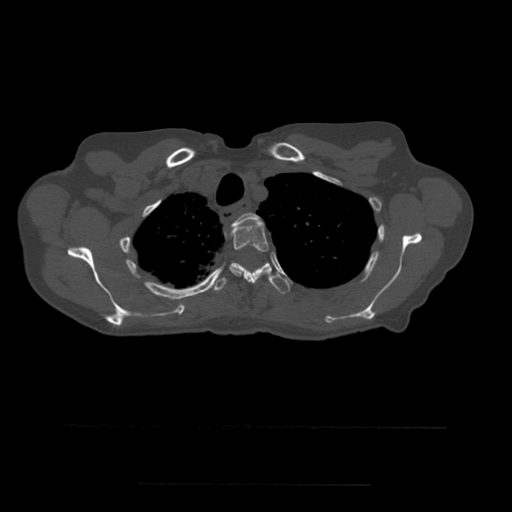
CT including the spine, one axial slice. Slice 417 of 544 in the series (ordered by position). Bone window (W 1800 / L 400 HU). 1.25 mm slice thickness. 512 × 512 image matrix, field of view 350 × 350 mm. Patient age 58 years. Case-level facts recorded for this patient, not image findings: primary cancer: lung.
Outlined on this slice (semi-automatic segmentation, software-assisted and operator-edited):
- T2 vertebra: box from (x=232, y=213) to (x=260, y=230) px
- T3 vertebra: (x=230, y=221)–(x=269, y=283)
- T4 vertebra: (x=211, y=263)–(x=290, y=294)